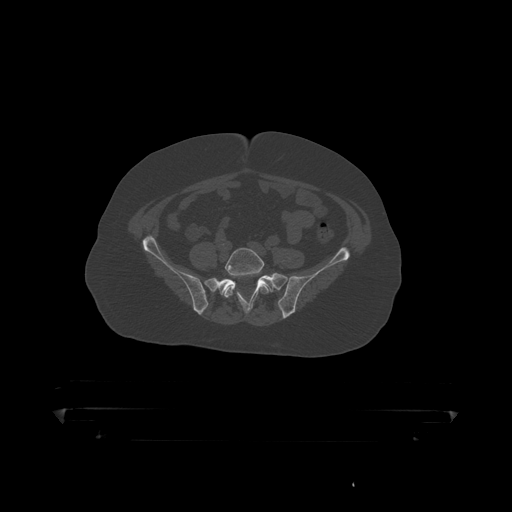
CT including the spine, one axial slice; slice 30 of 390 in the series (ordered by position); reconstruction kernel STANDARD; 120 kVp; bone window (W 1800 / L 400 HU); 1.25 mm slice thickness; 512 × 512 image matrix, field of view 650 × 650 mm. Patient: male, 60 years. Case-level facts recorded for this patient, not image findings: primary cancer: prostate.
Annotated regions visible in this slice (semi-automatically segmented with operator editing):
- L5 vertebra: box from (x=224, y=248) to (x=270, y=298) px